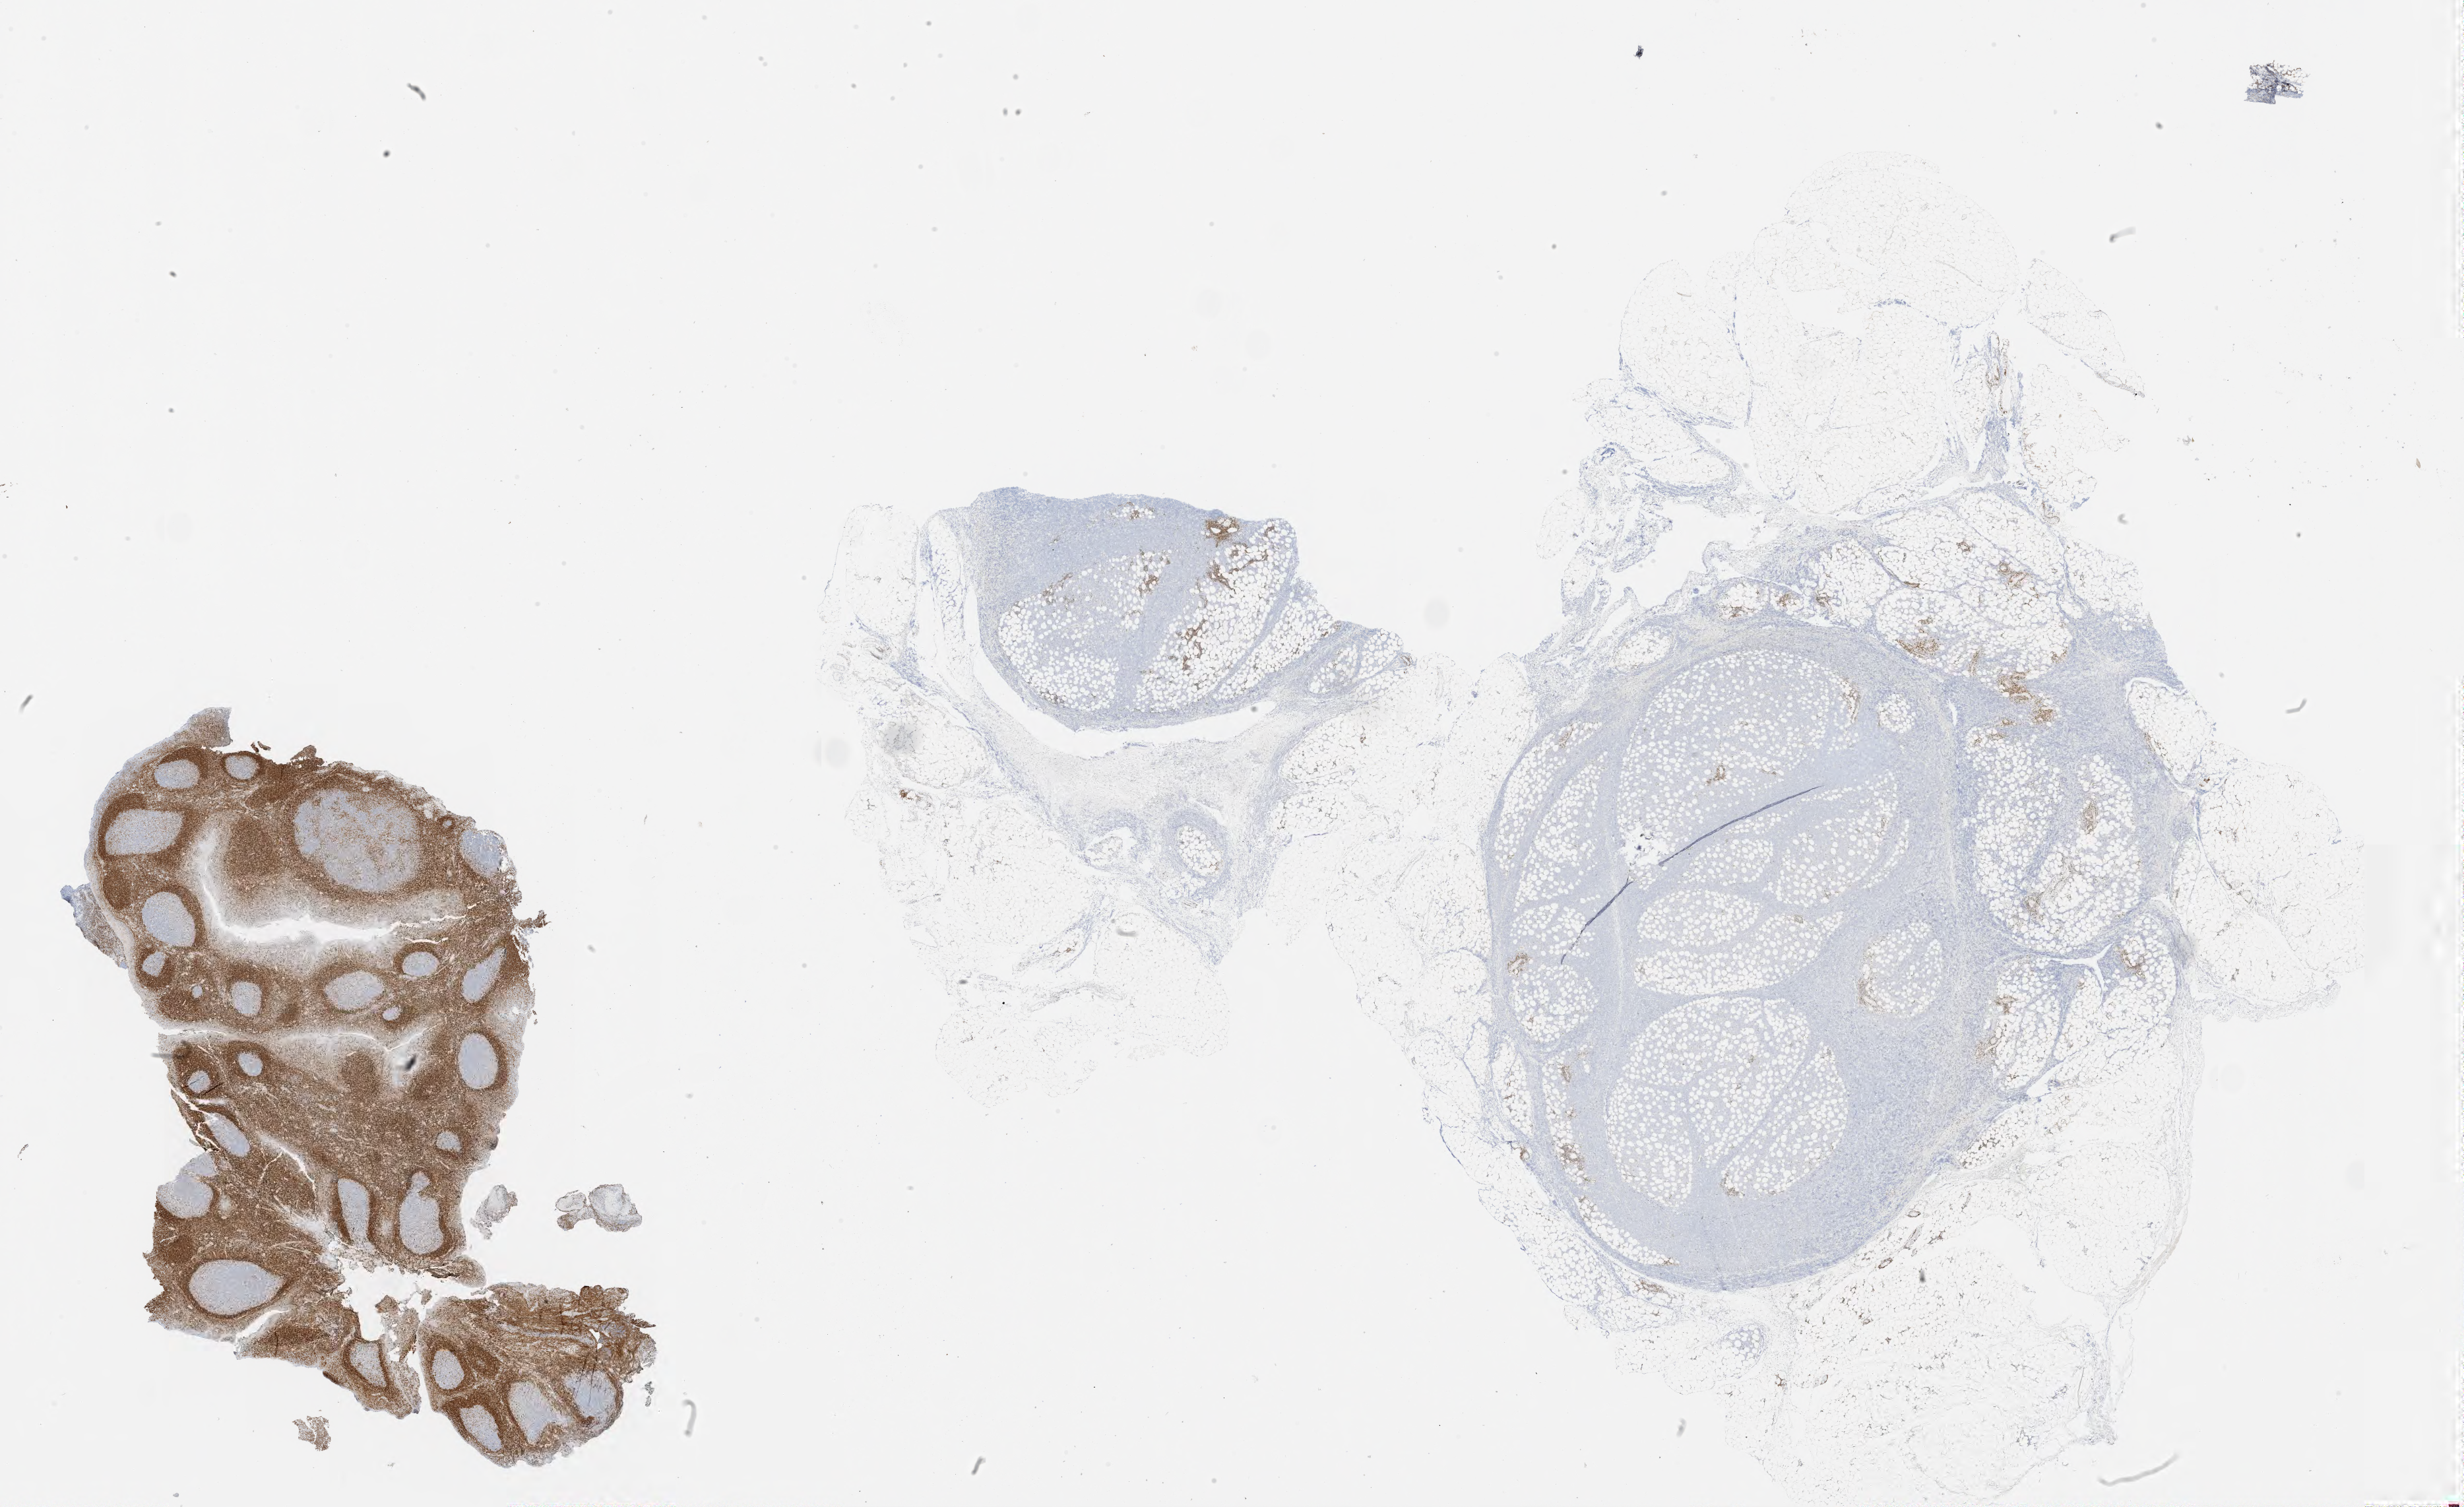
Immunohistochemistry (IHC) whole-slide image stained for BCL2 — shown as a low-resolution overview of the whole scanned area (about 30.0 x 18.3 mm), specimen: tumor tissue. Male patient, age 24 years.
Diagnosis: Burkitt lymphoma, NOS.